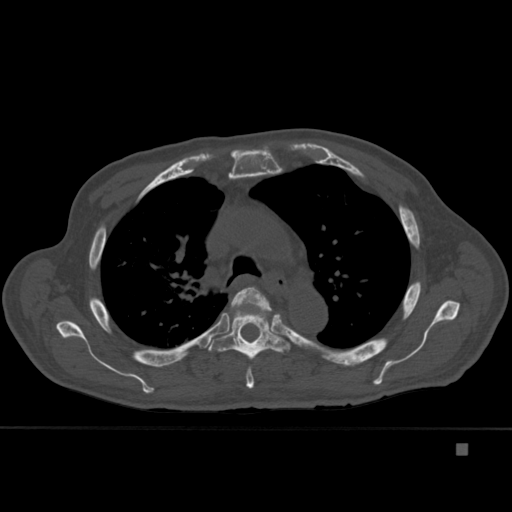
CT including the spine, one axial slice; slice 311 of 451 in the series (ordered by position); bone window (W 1800 / L 400 HU); 1.5 mm slice thickness; 512 × 512 image matrix, field of view 378 × 378 mm. Male patient, age 75 years. From the clinical record (not read from this slice): primary cancer: prostate.
Structures marked on this image (semi-automatic segmentation, software-assisted and operator-edited):
- T4 vertebra: bounding box (x1, y1, x2, y2) in pixels: (225, 287, 276, 389)
- T5 vertebra: (208, 304, 290, 360)